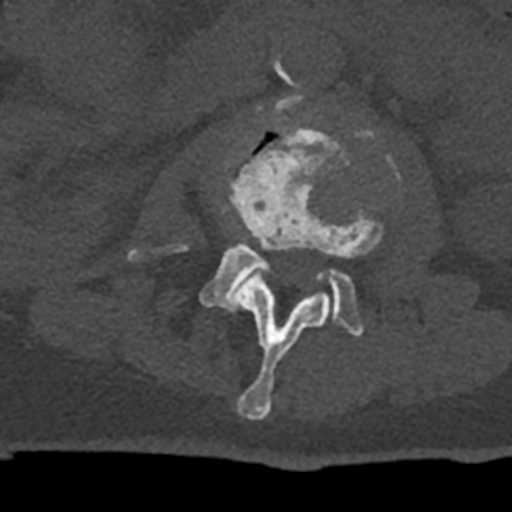
CT including the spine, one axial slice; slice 352 of 797 in the series (ordered by position); reconstruction kernel Br40s/3; bone window (W 1800 / L 400 HU); 0.5 mm slice thickness; 512 × 512 image matrix. Male patient, age 74 years. Case-level facts recorded for this patient, not image findings: primary cancer: renal.
Outlined on this slice (semi-automatic segmentation, software-assisted and operator-edited):
- L2 vertebra: bounding box [x1, y1, x2, y2] px = [218, 124, 384, 420]
- L3 vertebra: [129, 96, 362, 336]